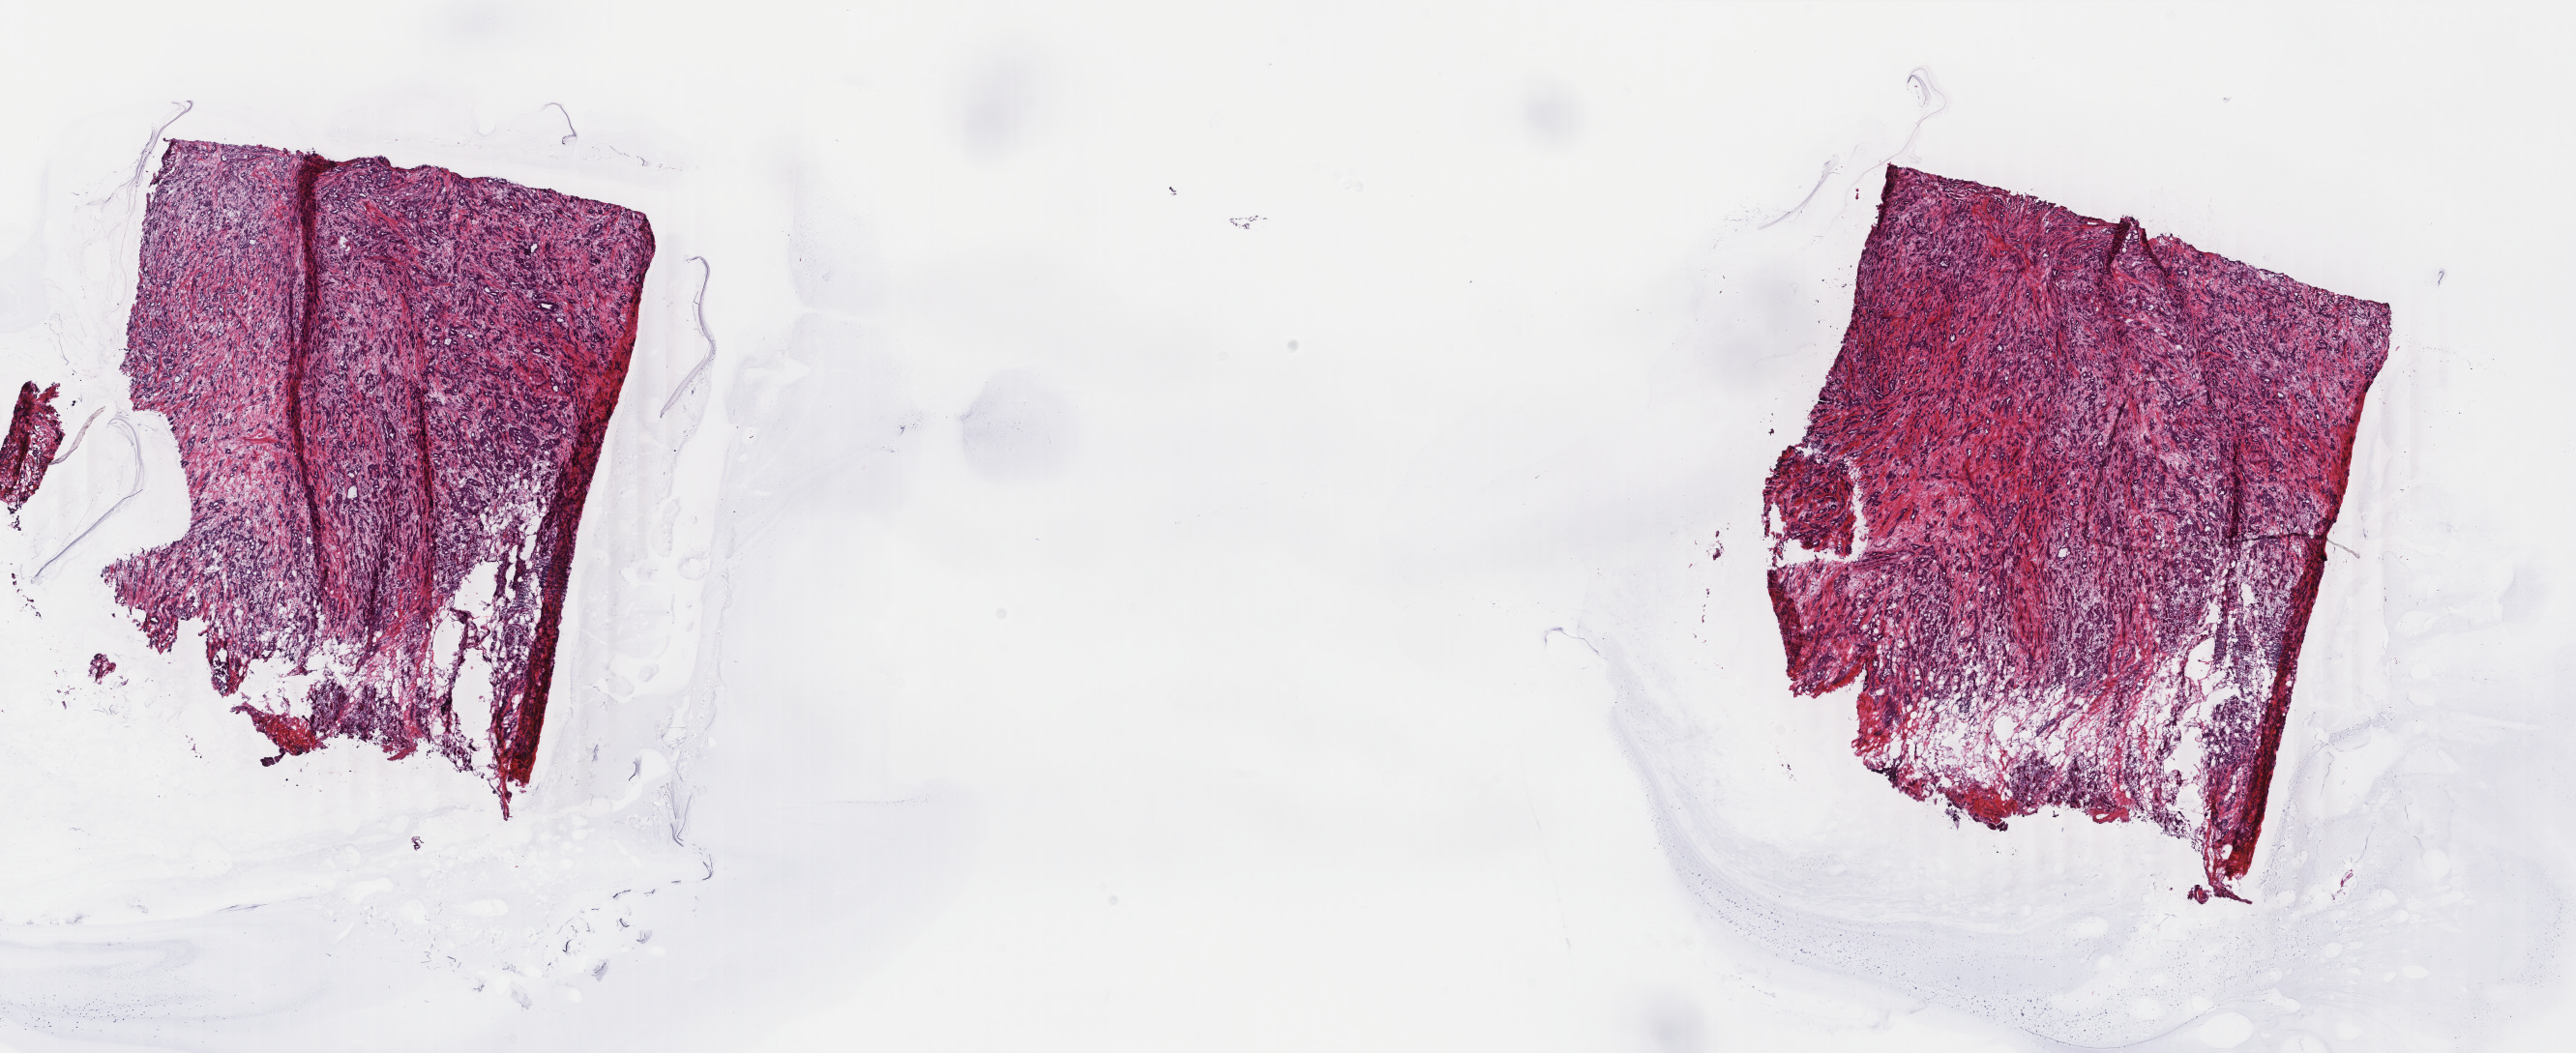
Digitized H&E tissue section (whole slide) — whole scanned area (about 21.2 x 8.7 mm) shown as a low-resolution overview; frozen section; primary tumour sample from the breast. Patient: female, age at initial diagnosis 49 years. Slide review estimates, as recorded: tumour cells 100%, tumour nuclei 95%, normal cells 0%, stromal cells 0%, necrosis 0%. Infiltration values recorded for this section: lymphocyte infiltration 0%, monocyte infiltration 0%, neutrophil infiltration 0%.
Lymph nodes positive (case pathology): 2 of 19 examined. Histologic diagnosis: Infiltrating duct carcinoma, NOS. Laterality: left. AJCC pathologic stage: IIB.